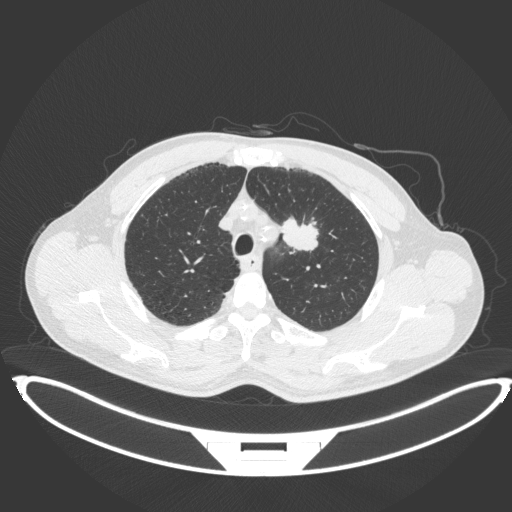
Chest CT, one axial slice; position 343 of 407 along the scan axis; reconstruction kernel B31f; lung window (W 1500 / L -600 HU); 512 × 512 image matrix, field of view 457 × 457 mm. Patient: male, 60 years. Case-level facts recorded for this patient, not image findings: clinical TNM (as recorded): T2a N0 M0; histopathological grade: G1-G2.
Annotated regions visible in this slice (rectangle marked by the reading radiologist):
- lung tumour (recorded histology: squamous cell carcinoma): bounding box [x1, y1, x2, y2] px = [279, 212, 321, 255]